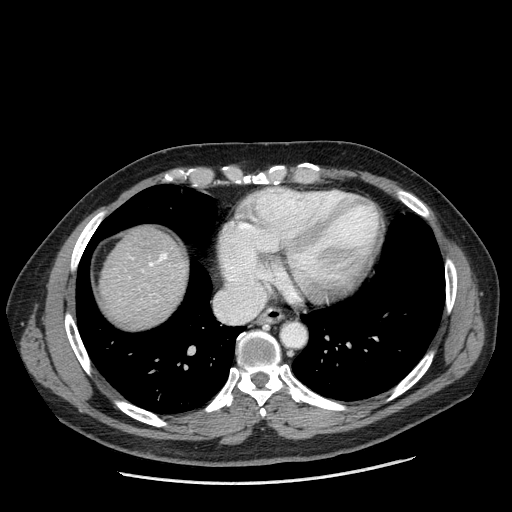
Contrast-enhanced abdominal CT (liver protocol), one axial slice. Position 177 of 198 along the scan axis. Reconstruction kernel STANDARD. One of 2 acquisitions stored at this slice position. Soft-tissue window (W 400 / L 40 HU). 2.5 mm slice thickness. 512 × 512 image matrix, field of view 400 × 400 mm. Case-level facts recorded for this patient, not image findings: diagnosis: hepatocellular carcinoma (patient treated with transarterial chemoembolisation; whether this scan precedes or follows treatment is not stated here); TNM stage (as recorded): Stage-II; Child-Pugh class: A; tumour nodularity: multinodular; tumour size: 2.6 cm.
Annotated regions visible in this slice (semi-automatic segmentation, software-assisted and operator-edited):
- liver parenchyma outside the tumour (the mass and vessels are separate outlines, so this box may not span the whole liver): bounding box [x1, y1, x2, y2] px = [100, 226, 188, 328]
- liver vessels: [130, 253, 167, 271]